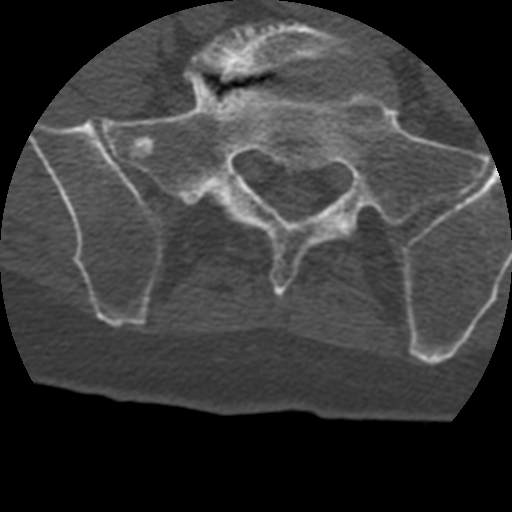
CT including the spine, one axial slice. Slice 27 of 399 in the series (ordered by position). 120 kVp. Bone window (W 1800 / L 400 HU). 1.25 mm slice thickness. 512 × 512 image matrix, field of view 160 × 160 mm. Patient age 69 years. From the clinical record (not read from this slice): primary cancer: prostate.
Annotated regions visible in this slice (semi-automatic segmentation, software-assisted and operator-edited):
- L5 vertebra: bounding box [x1, y1, x2, y2] px = [191, 22, 355, 203]